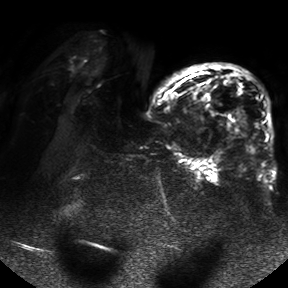
Breast MRI, one axial slice. Position 21 of 50 along the scan axis. Diffusion-weighted series; image 2 of 4 stored at this slice position (different b-values; order by instance number). 1.5 T. 4 mm slice thickness. 288 × 288 image matrix, field of view 390 × 390 mm. Female patient.
Structures marked on this image (expert manual segmentation):
- tumour on diffusion-weighted imaging: box from (x=229, y=108) to (x=247, y=133) px